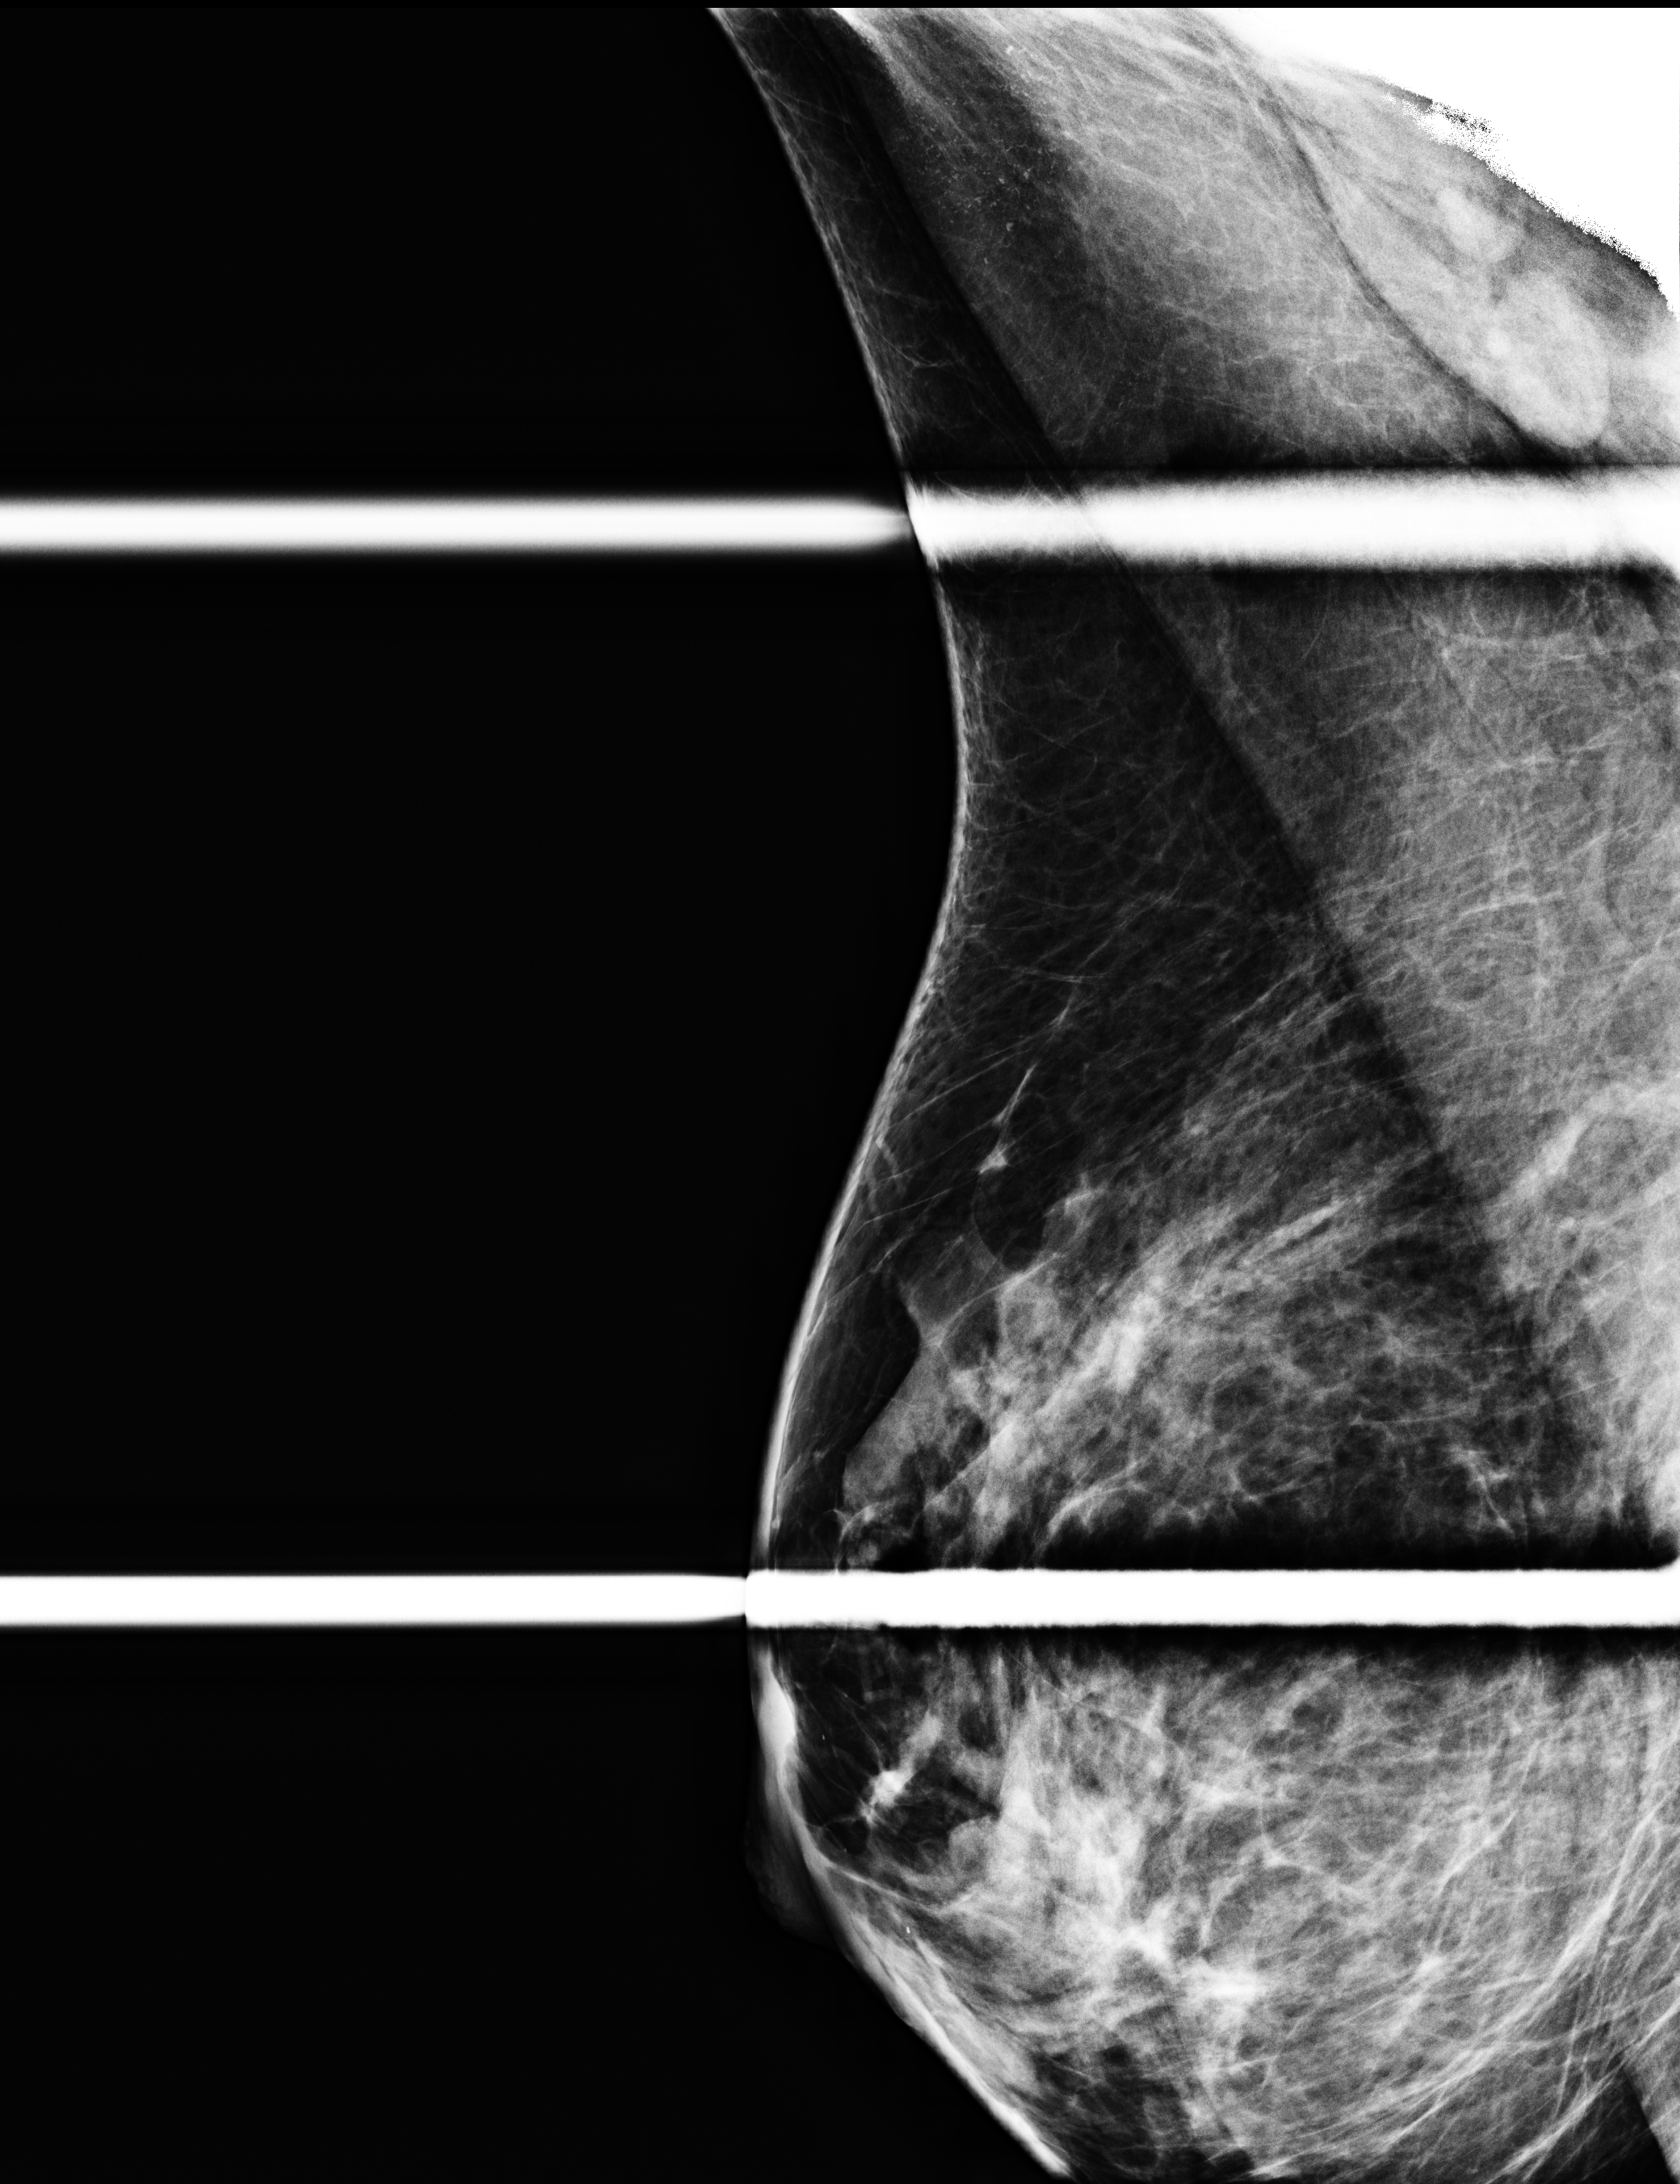
Additional work-up view. Patient: female, 45 years.
Image type: full-field digital mammogram. Breast: right. Projection: MLO view, spot compression.